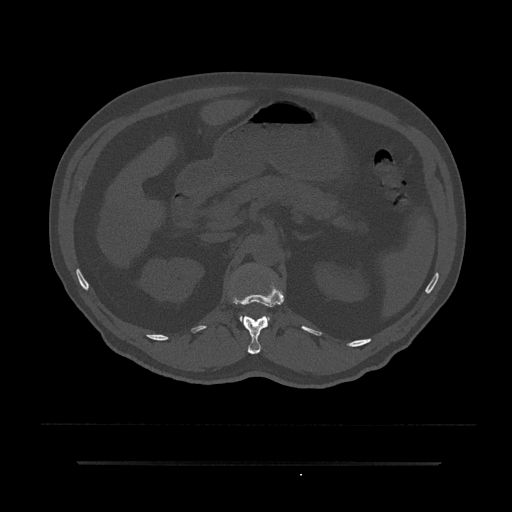
CT including the spine, one axial slice; position 186 of 797 along the scan axis; reconstruction kernel Br40s/3; bone window (W 1800 / L 400 HU); 0.5 mm slice thickness; 512 × 512 image matrix, field of view 464 × 464 mm. Male patient, age 59 years. From the clinical record (not read from this slice): primary cancer: bile ducts.
Annotated regions visible in this slice (semi-automatically segmented with operator editing):
- L1 vertebra: bounding box <240,316,269,320> (left, top, right, bottom; pixels)
- T12 vertebra: <231,279,284,354>